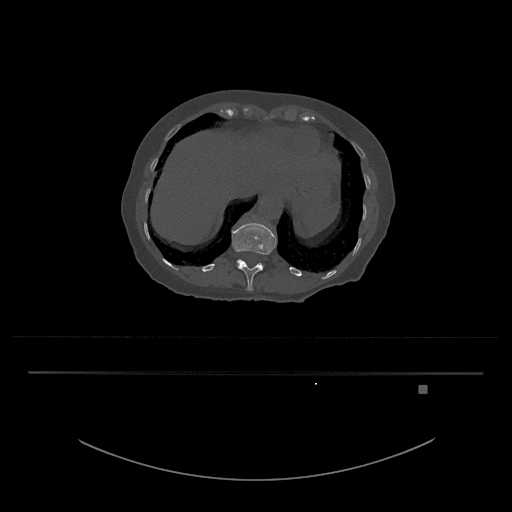
CT including the spine, one axial slice. Slice 601 of 797 in the series (ordered by position). Reconstruction kernel Br40s/3. 120 kVp. Bone window (W 1800 / L 400 HU). 0.5 mm slice thickness. 512 × 512 image matrix, field of view 500 × 500 mm. Patient: female, 57 years. Case-level facts recorded for this patient, not image findings: primary cancer: cervical.
Annotated regions visible in this slice (semi-automatically segmented with operator editing):
- T12 vertebra: bounding box (x1, y1, x2, y2) in pixels: (232, 223, 277, 291)